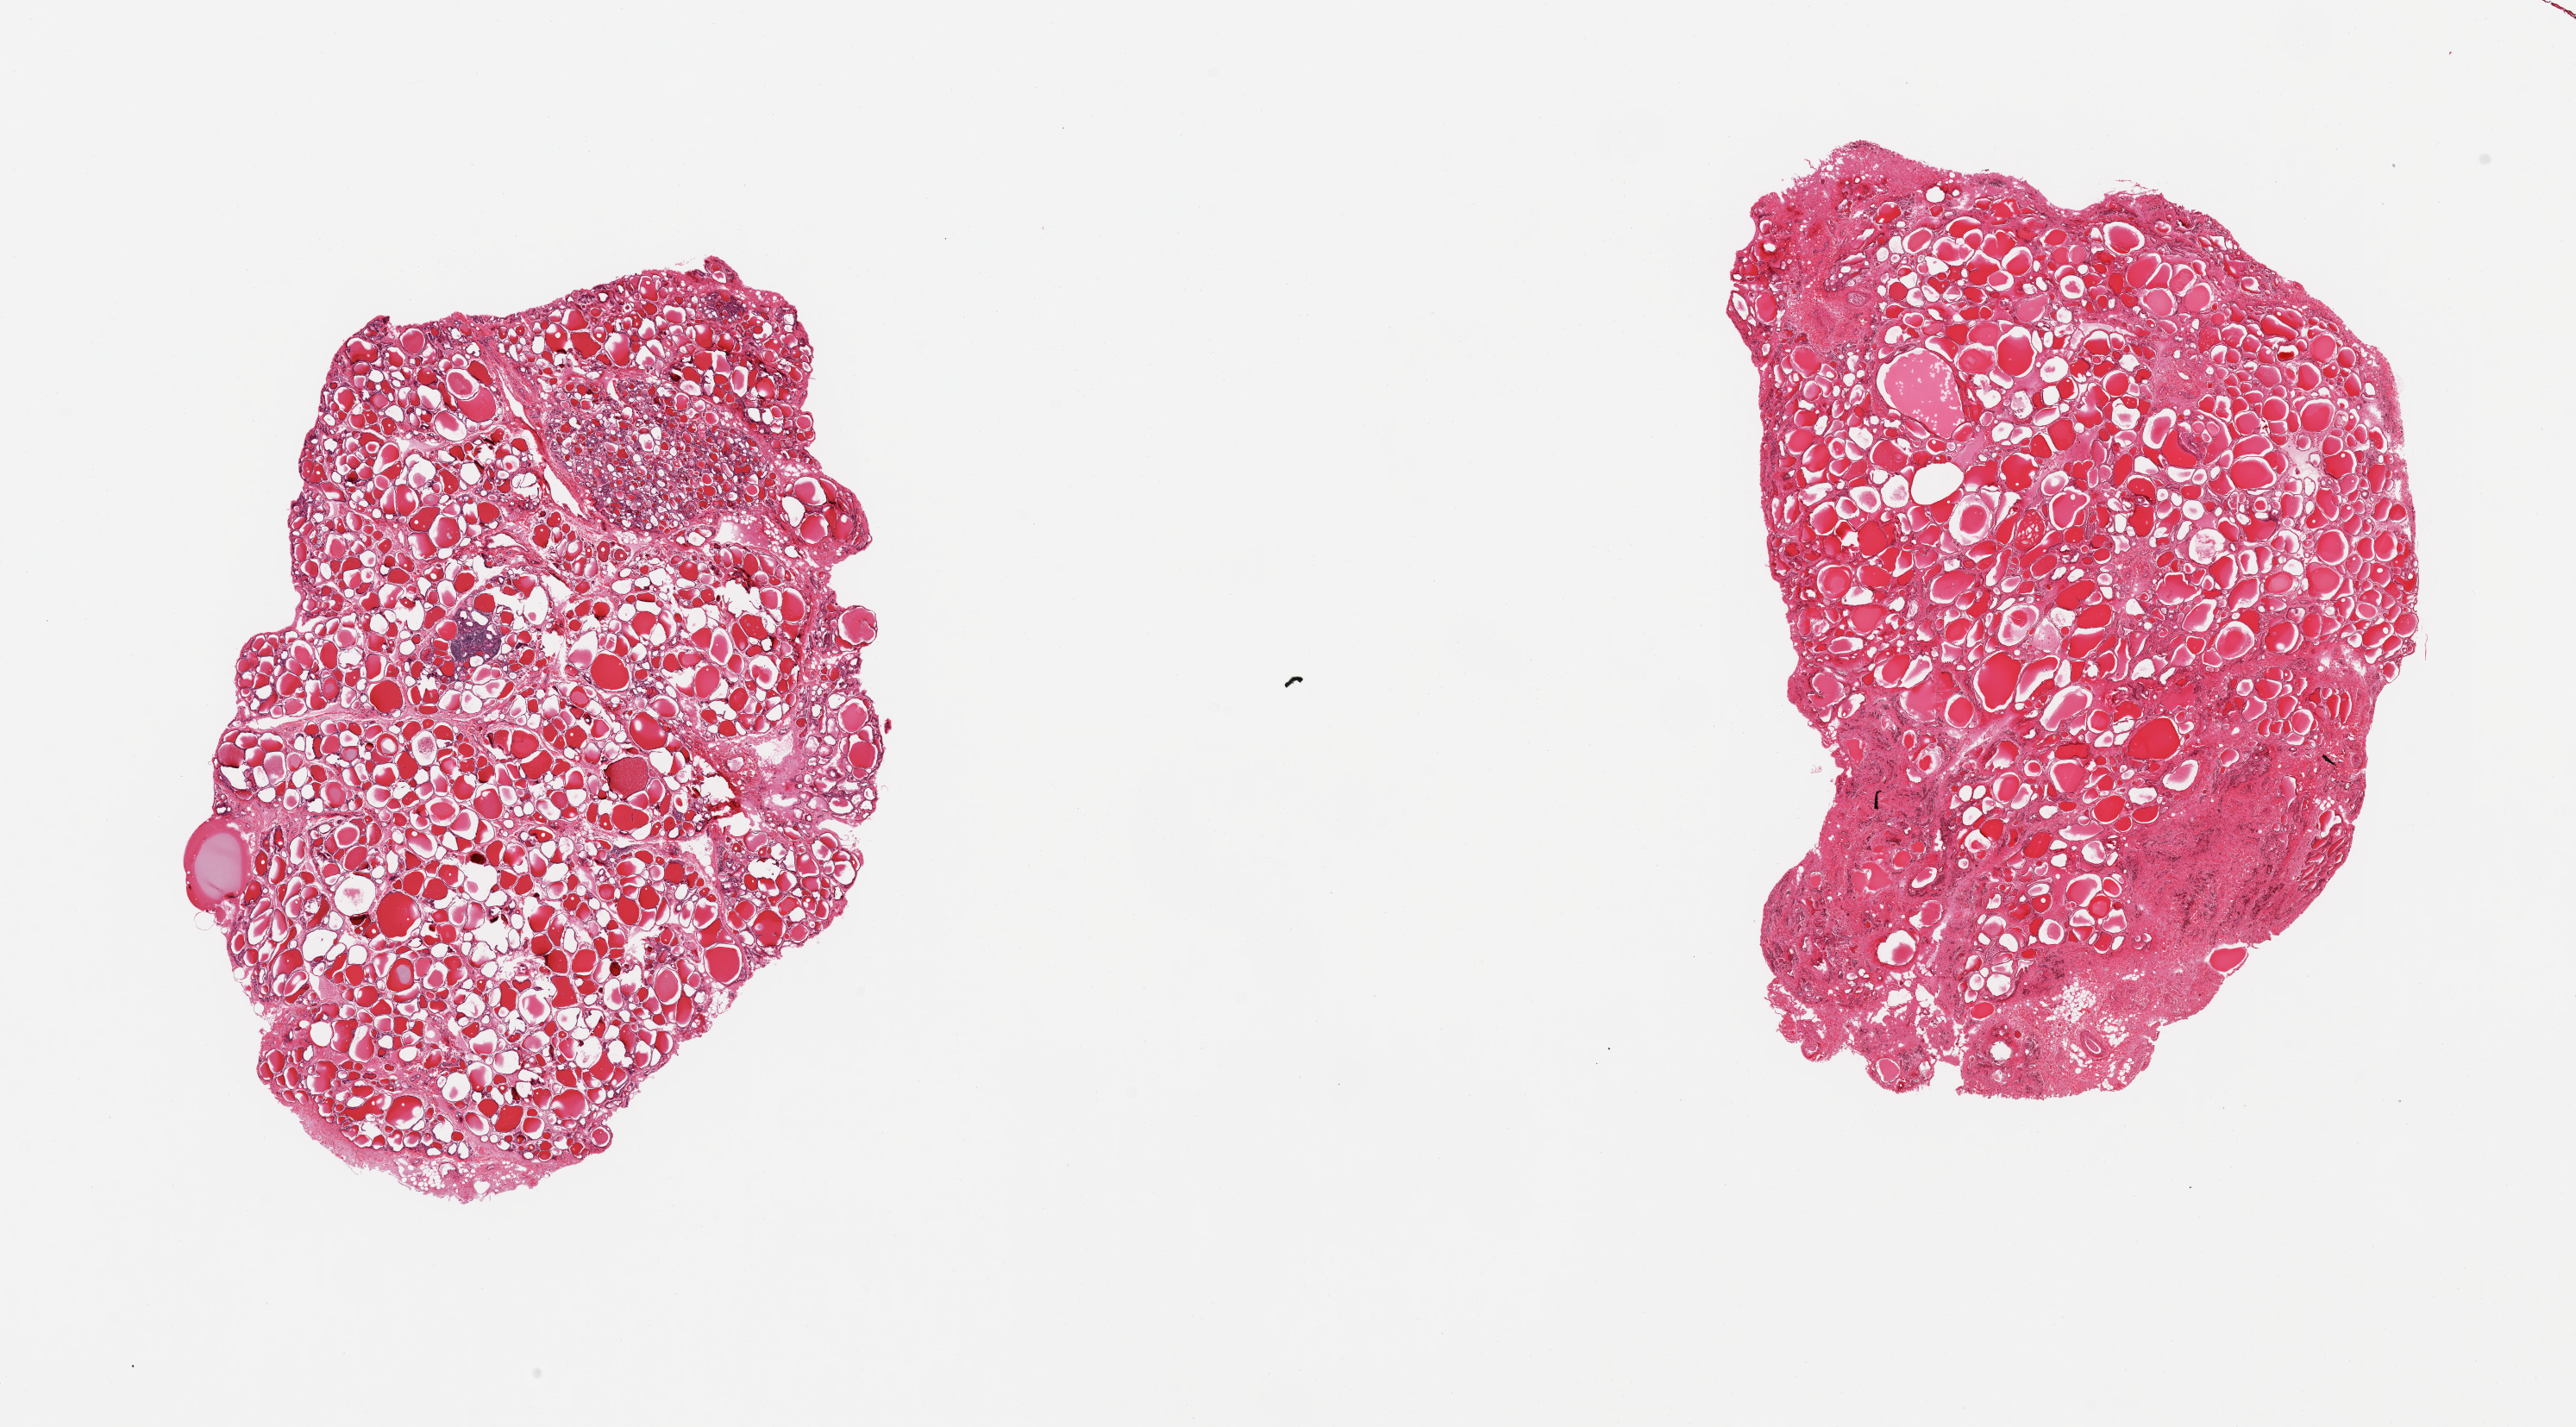
Digitized haematoxylin and eosin-stained section, brightfield, low-resolution overview of the scanned area, about 23.6 x 13.1 mm (acquisition: 20x scan), PAXgene-fixed, paraffin-embedded tissue, target tissue: thyroid, donor tissue sample. Donor sex: male.
Pathologist's review note for this sample: 2 pieces, single lymphoid aggregate, features of multinodular goiter.